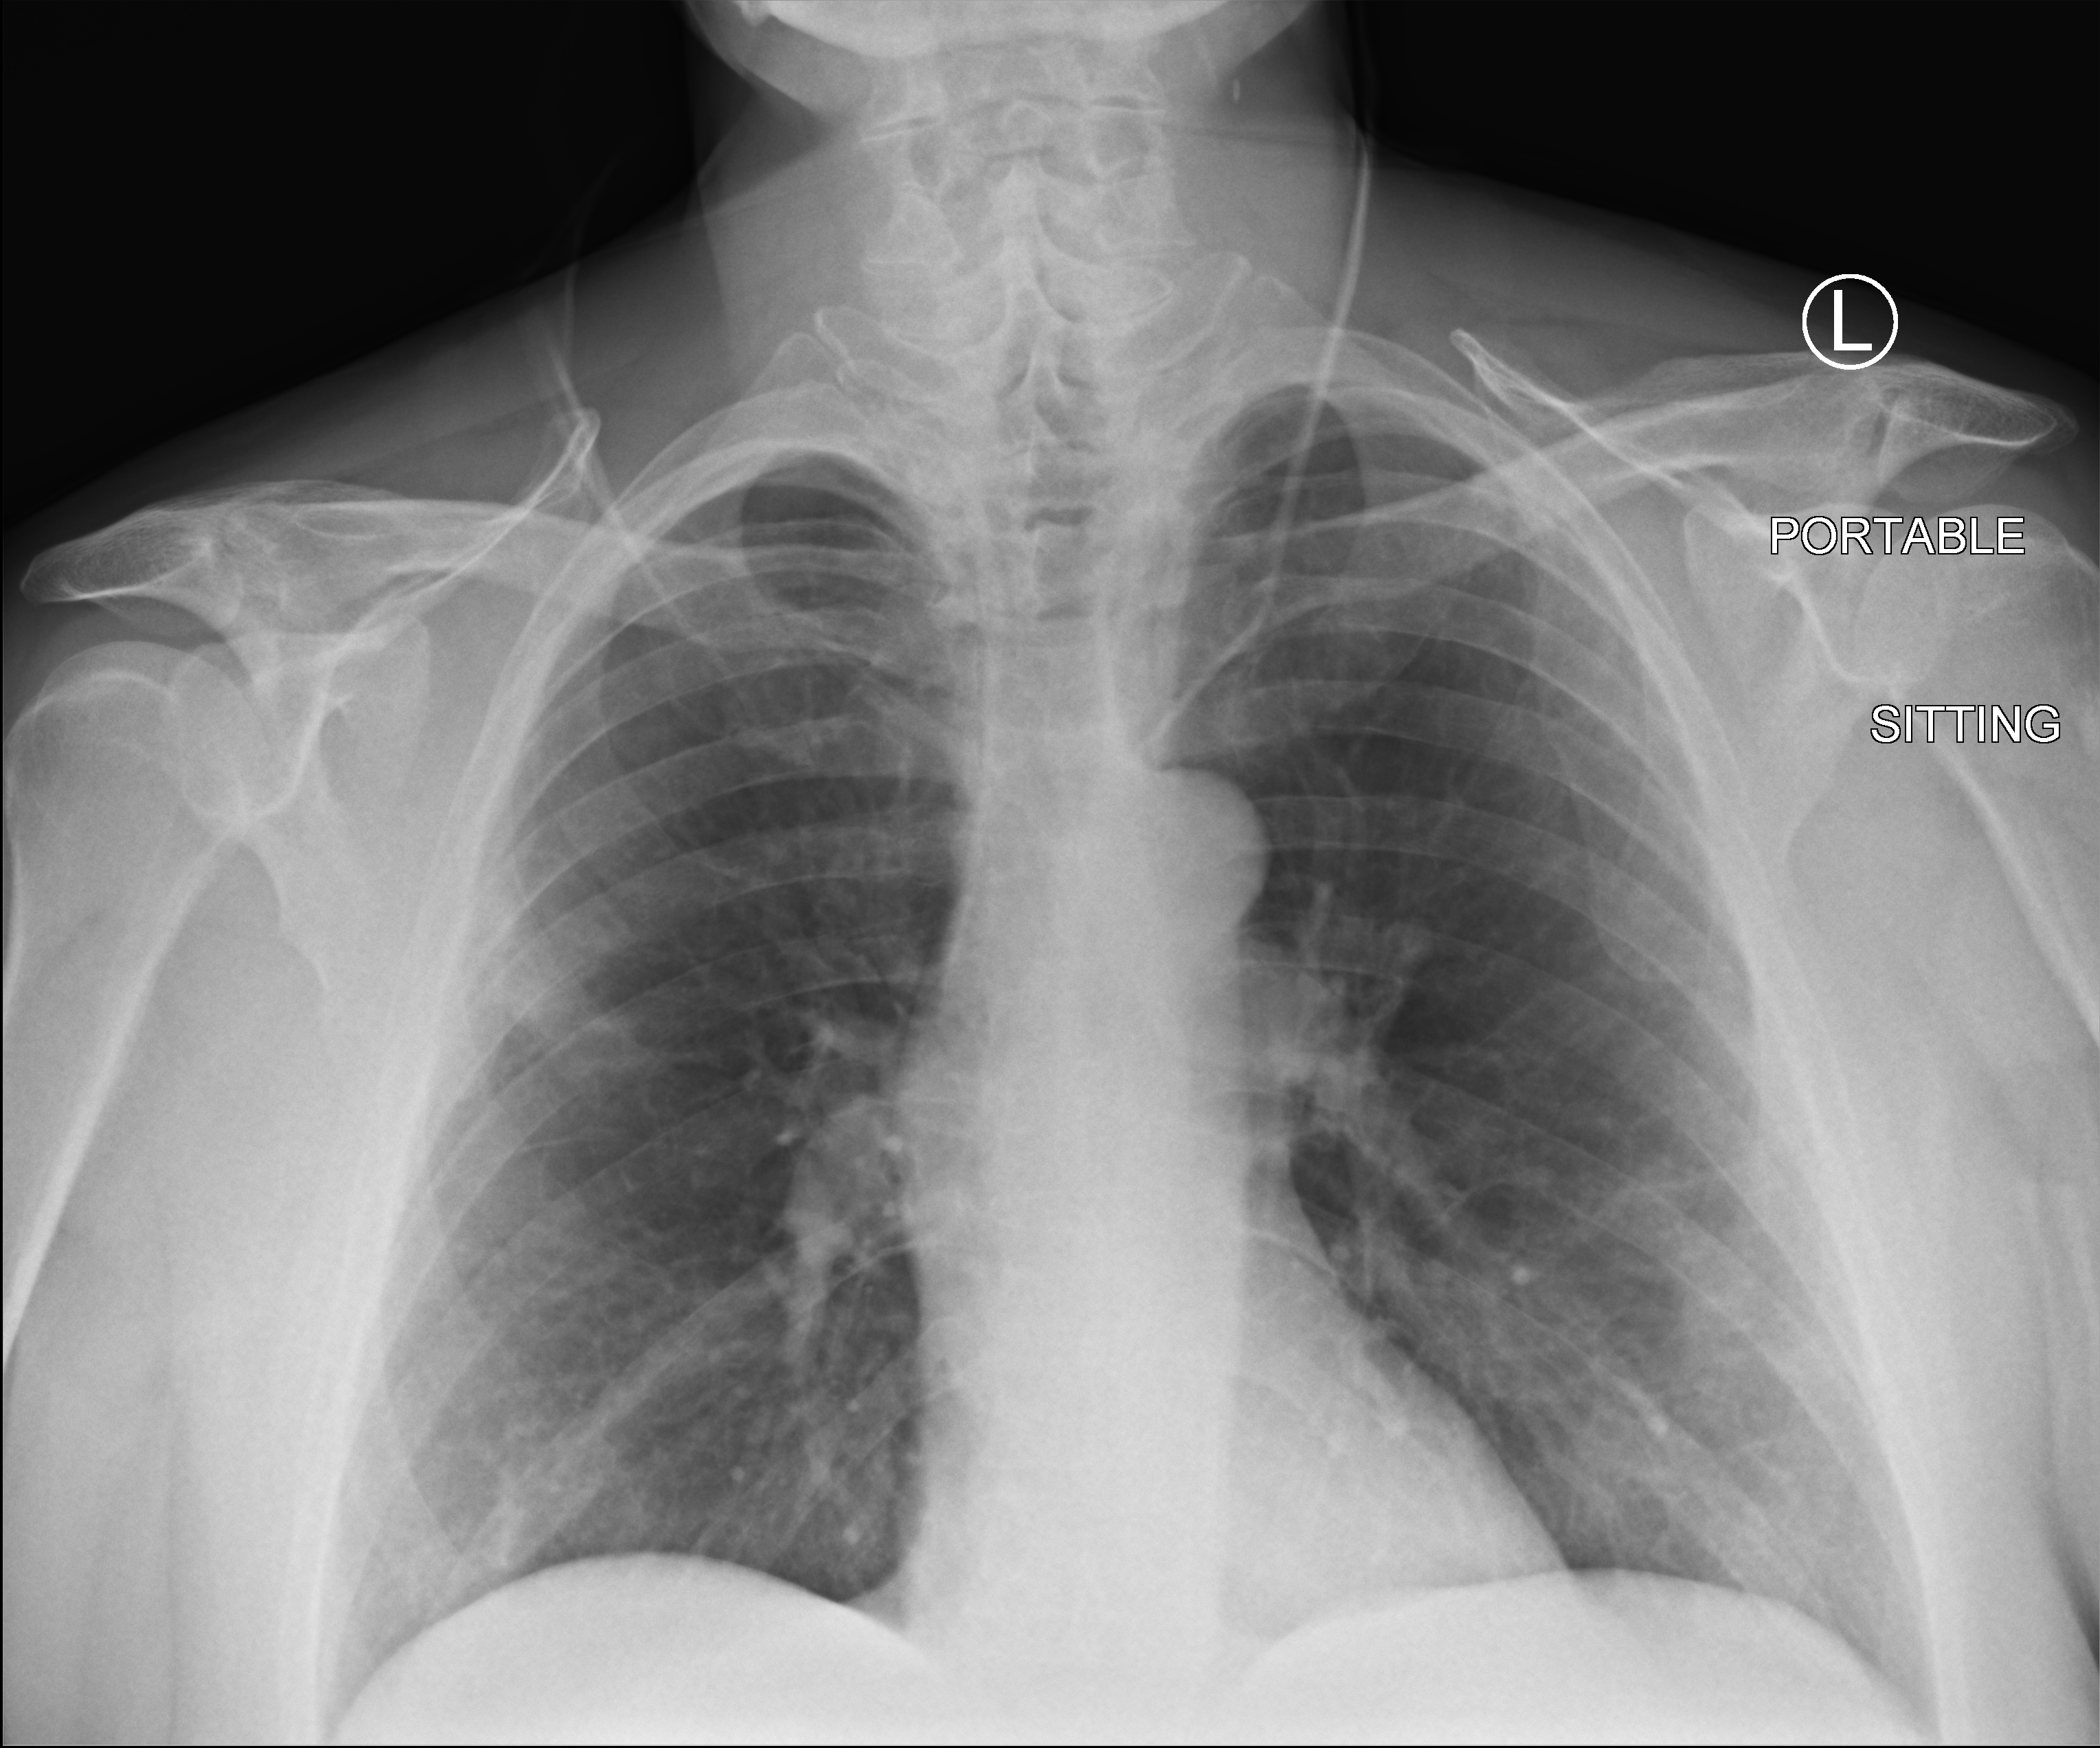
Portable chest radiograph; anteroposterior (AP) projection. Male patient hospitalised with COVID-19, age 60–74 years.
From the hospital-stay record, not from the radiograph (when in the stay this image was taken is not recorded): length of hospital stay: 2 days; mechanically ventilated during this hospital stay: no.